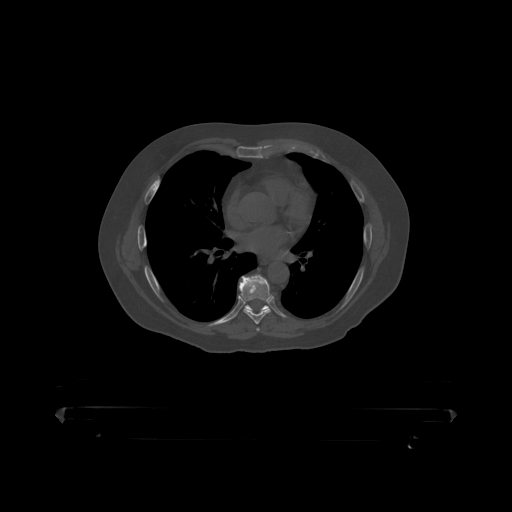
CT including the spine, one axial slice. Slice 273 of 390 in the series (ordered by position). Bone window (W 1800 / L 400 HU). 512 × 512 image matrix. Patient: male, 60 years. Case-level facts recorded for this patient, not image findings: primary cancer: prostate.
Structures marked on this image (semi-automatic segmentation, software-assisted and operator-edited):
- T7 vertebra: bounding box <239,275,273,319> (left, top, right, bottom; pixels)
- T8 vertebra: <245,305,270,311>